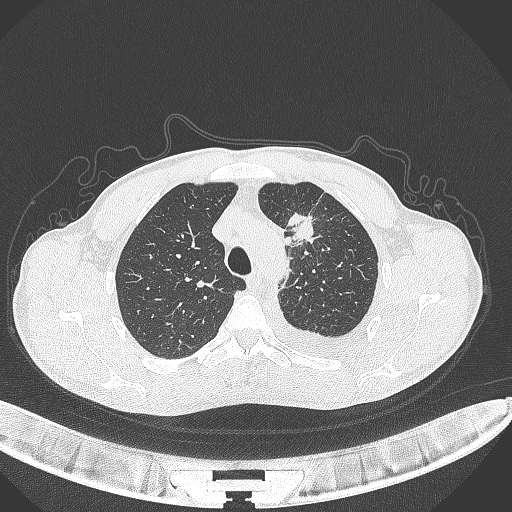
Chest CT, one axial slice; position 265 of 371 along the scan axis; reconstruction kernel B70f; 120 kVp; lung window (W 1500 / L -600 HU); 512 × 512 image matrix, field of view 400 × 400 mm. Male patient, age 49 years. Case-level facts recorded for this patient, not image findings: clinical TNM (as recorded): T1c N1 M1.
Outlined on this slice (bounding box drawn by a radiologist):
- lung tumour (recorded histology: adenocarcinoma): bounding box <286,209,315,247> (left, top, right, bottom; pixels)